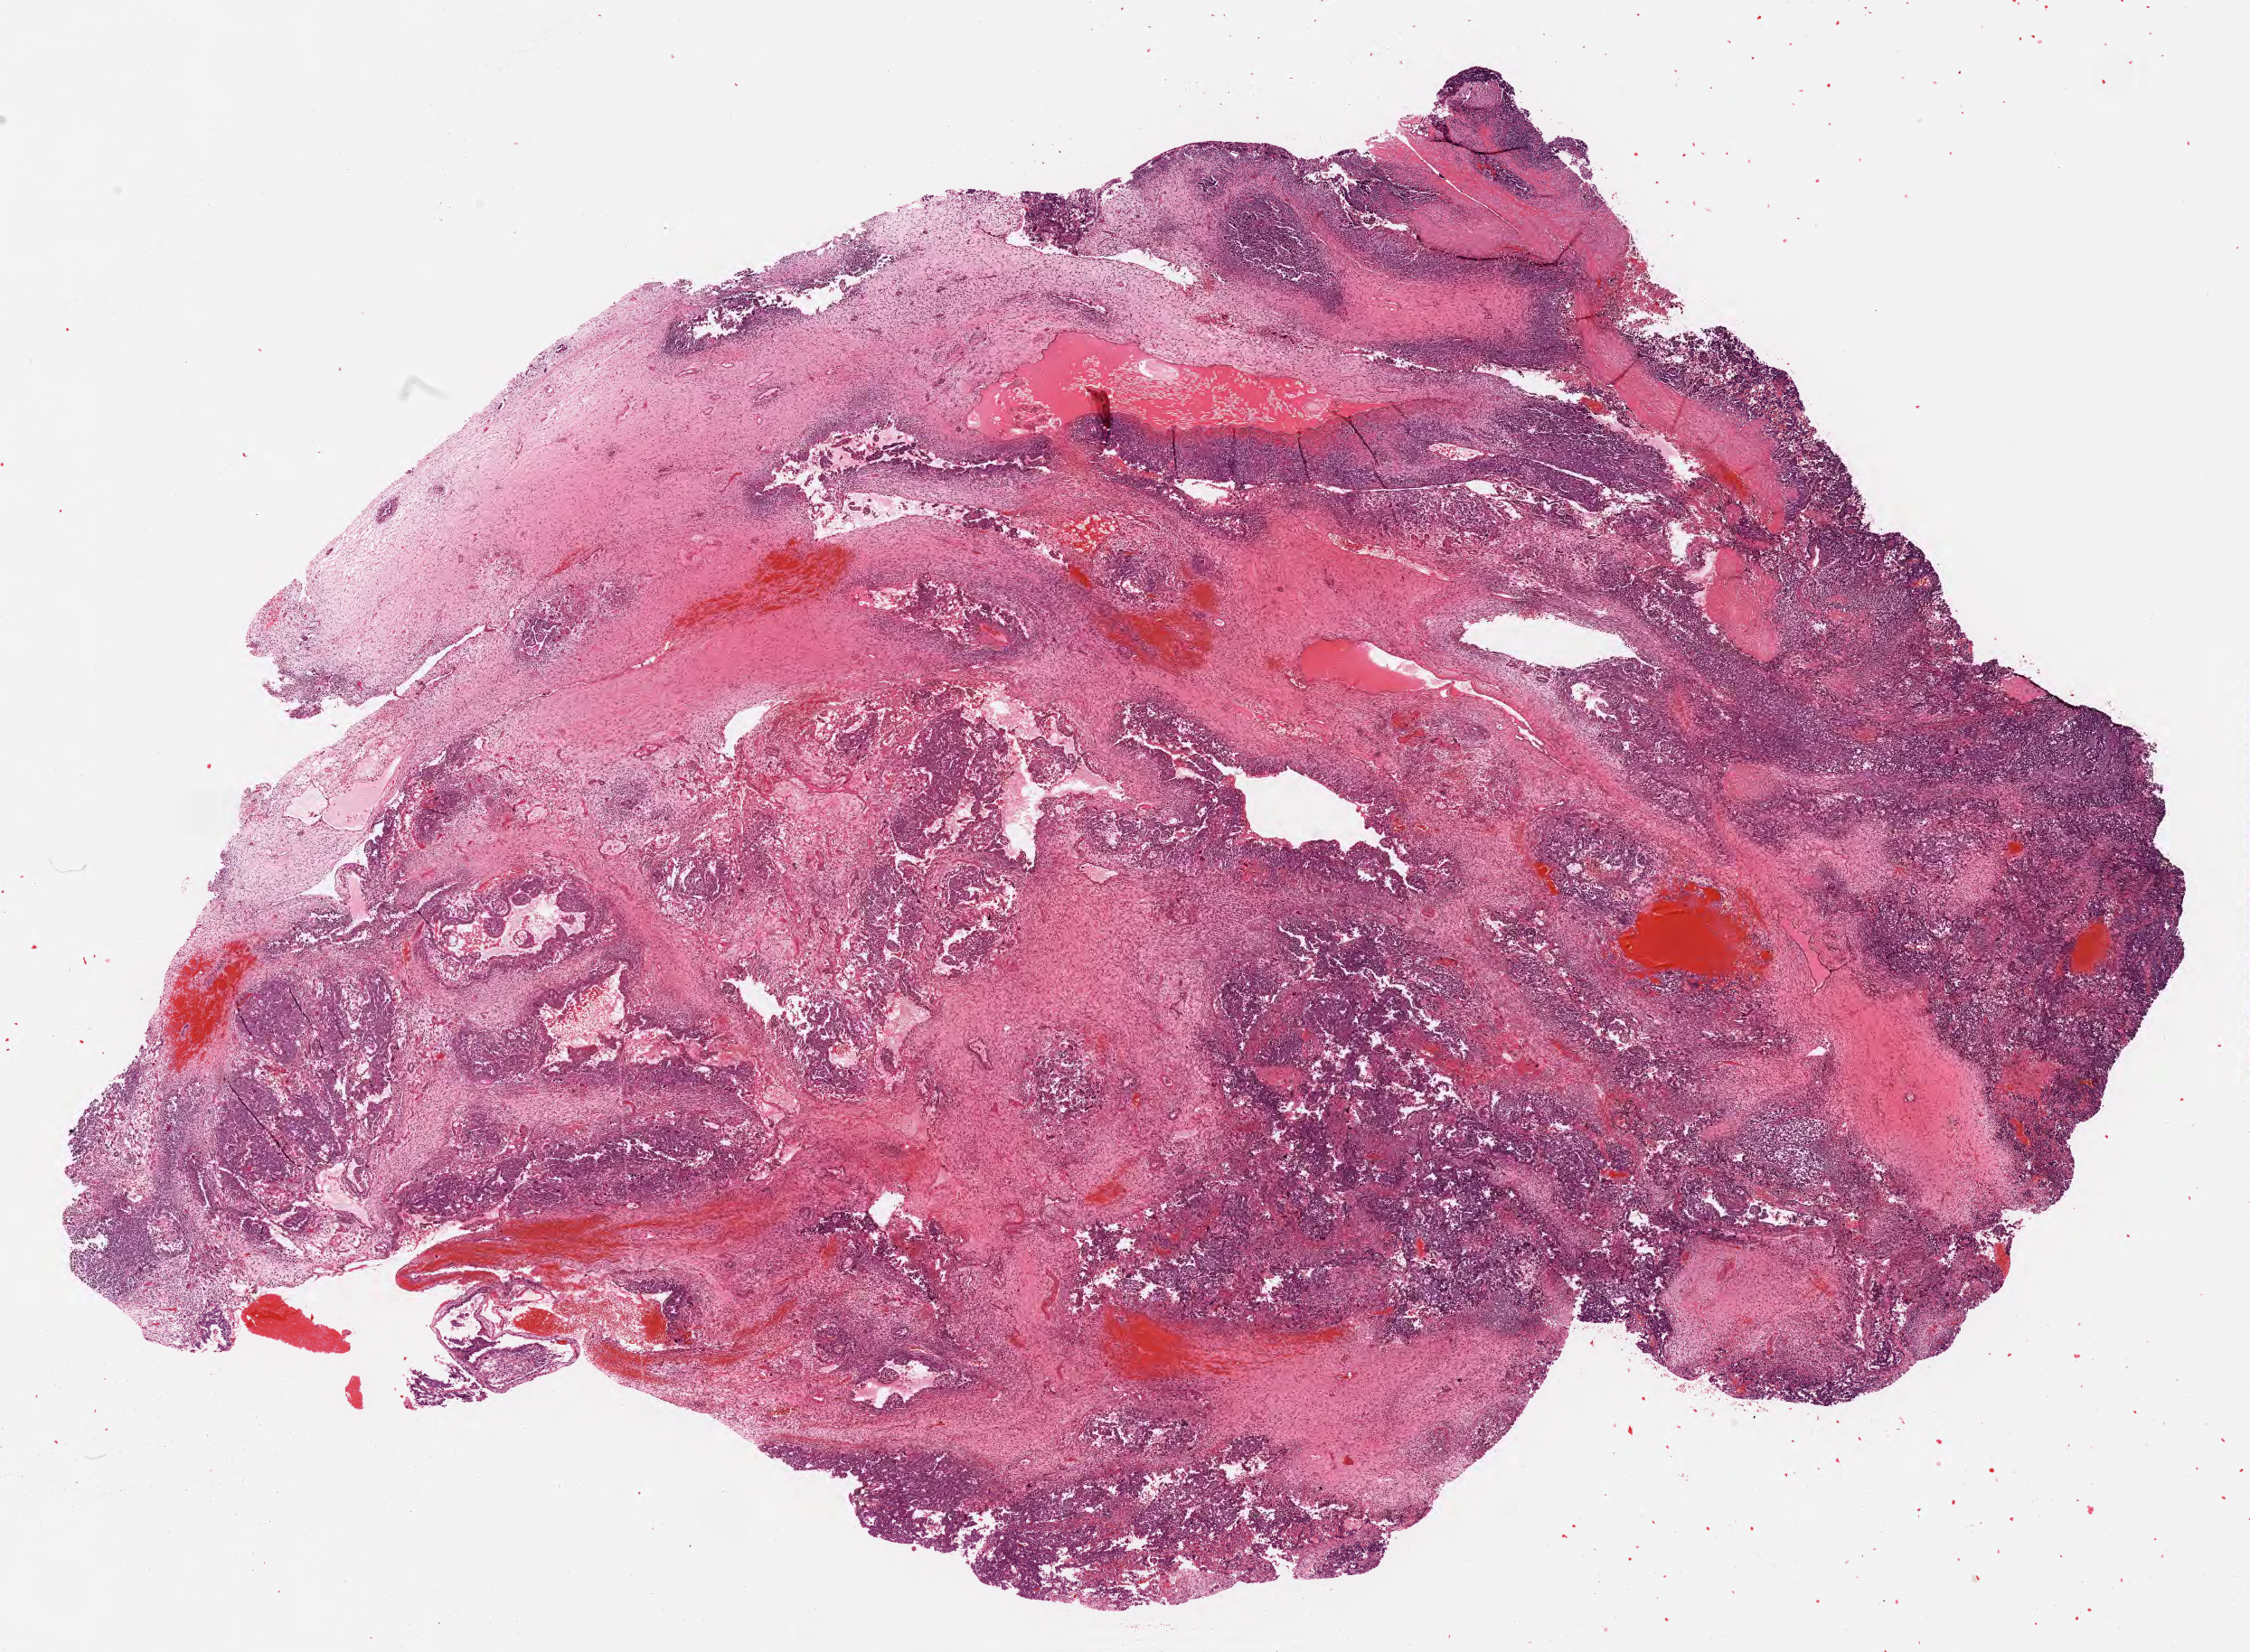
Whole-slide histology image, H&E, whole scanned area (about 19.7 x 14.4 mm, from a 20x scan) shown as a low-resolution overview, formalin-fixed paraffin-embedded (FFPE) diagnostic section, testis, primary tumour sample. Male patient; age at initial diagnosis 33 years.
- pathologic diagnosis: Mixed germ cell tumor
- AJCC pathologic stage: IS (7th edition)